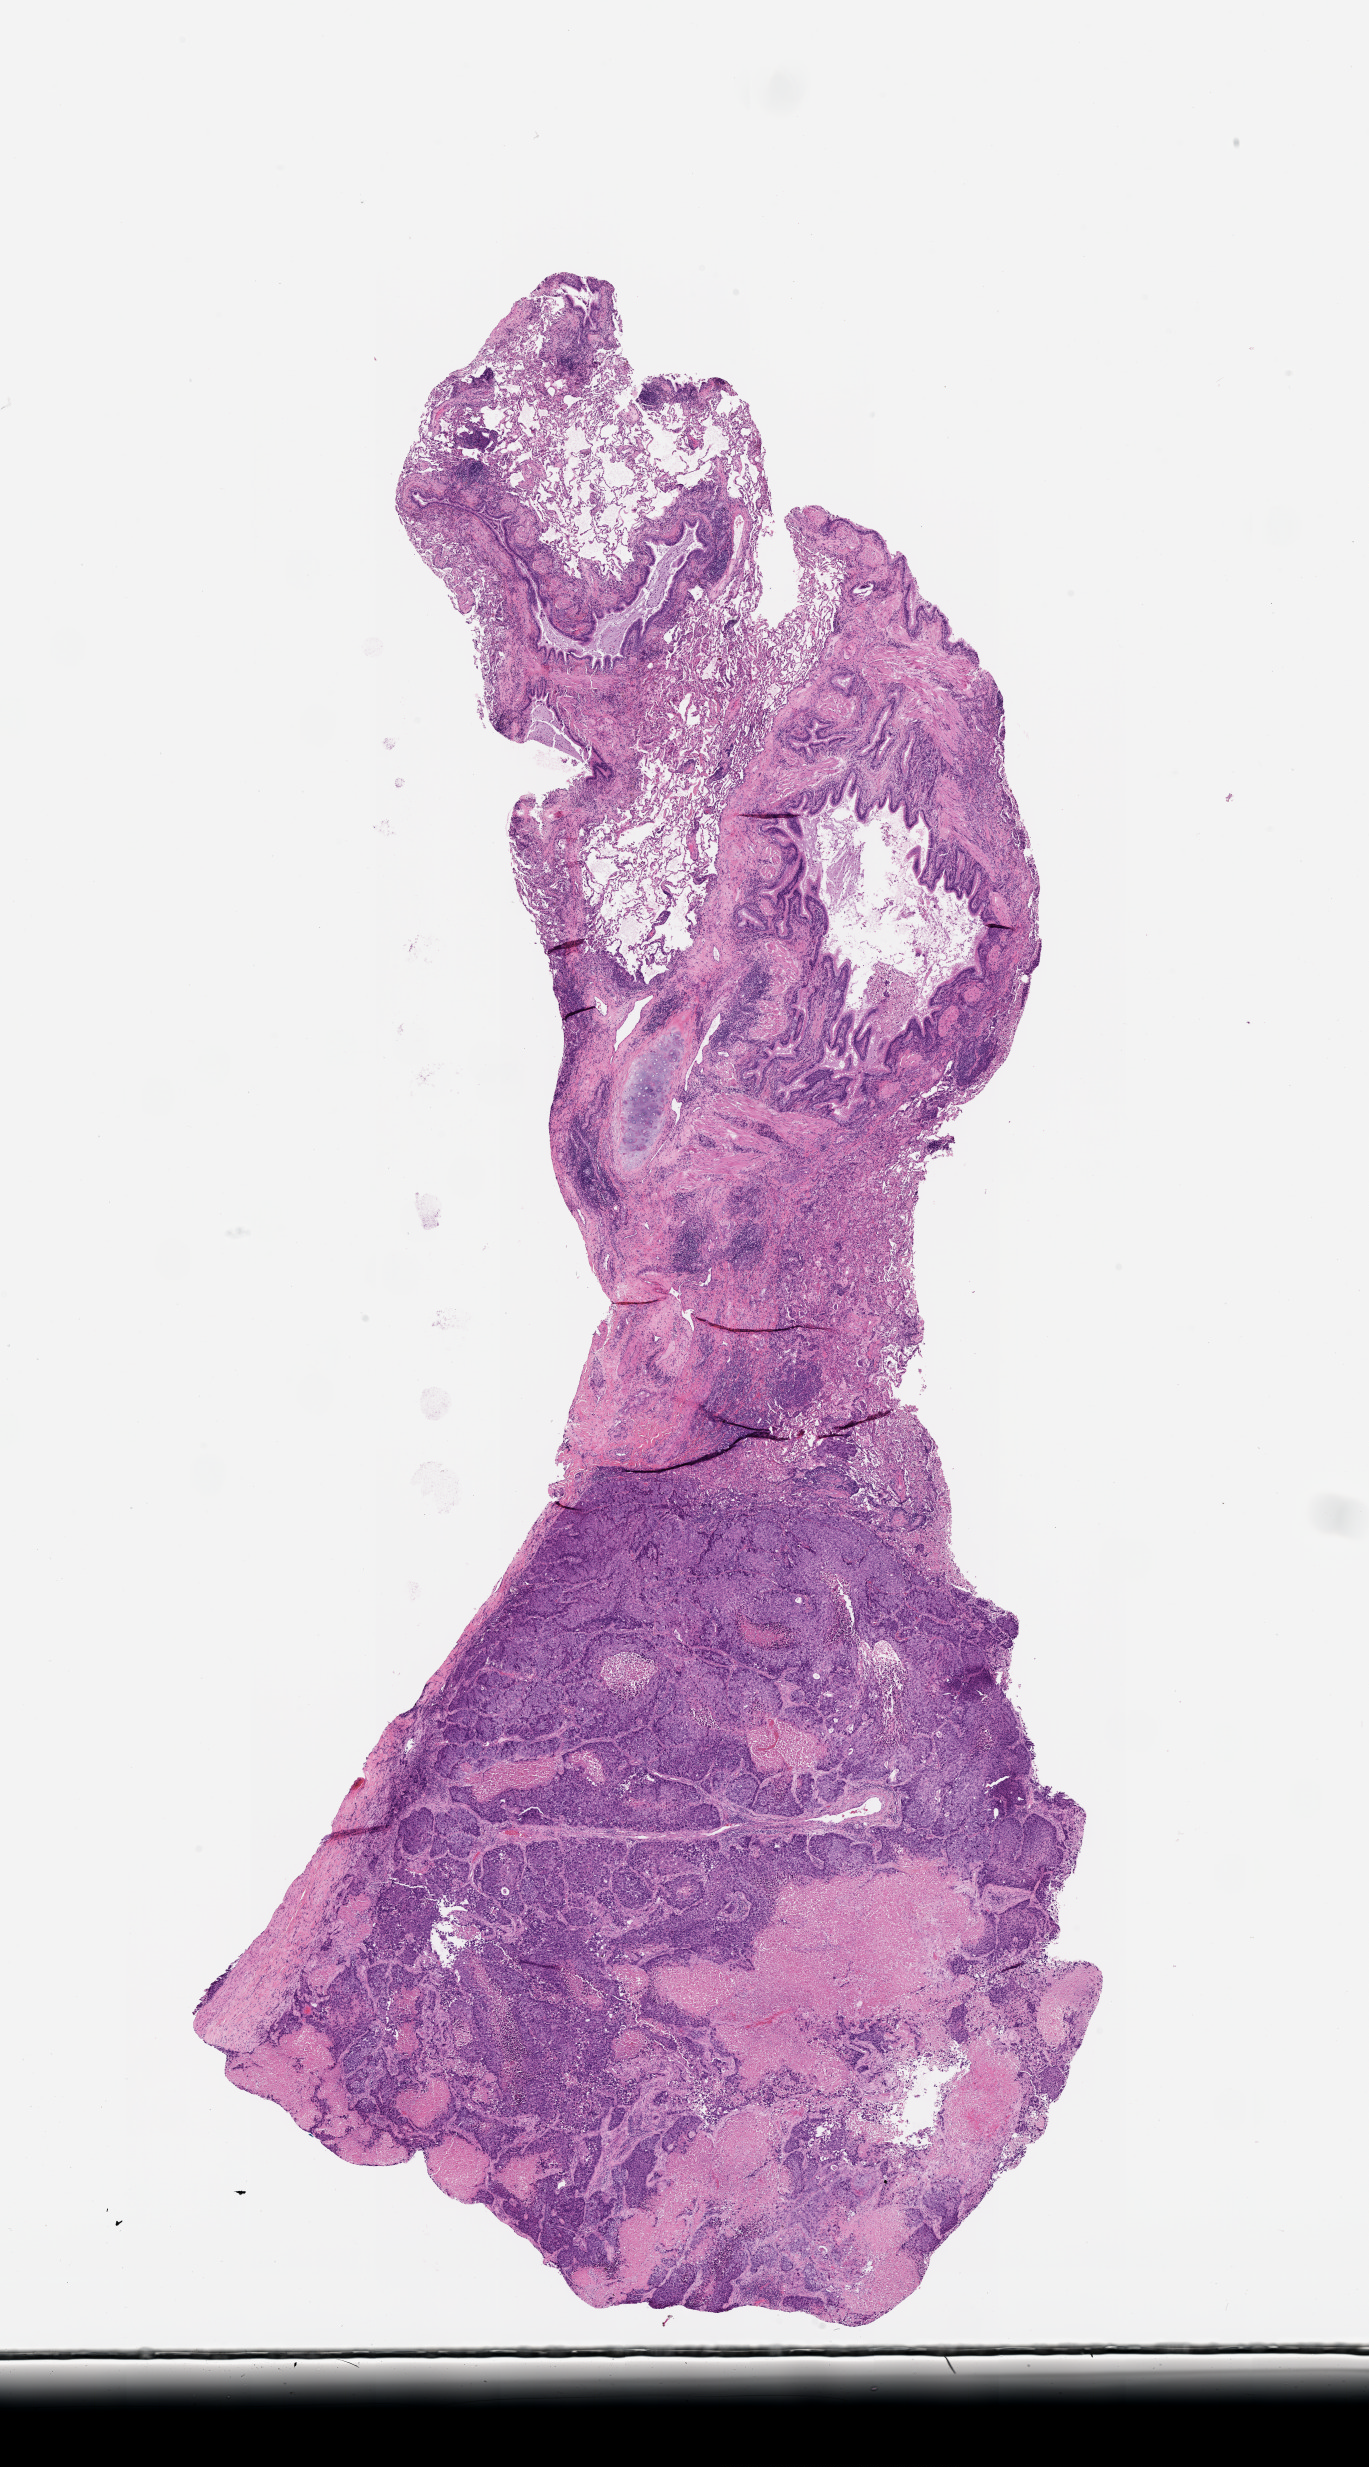
Digitized Hematoxylin and eosin (H&E) stained tissue section (whole slide), whole scanned area (about 11.0 x 19.9 mm) shown as a low-resolution overview; tumour tissue sample, lung. Patient: male, age 56 years.
Patient diagnosis (cohort enrolment): squamous cell carcinoma (lung).